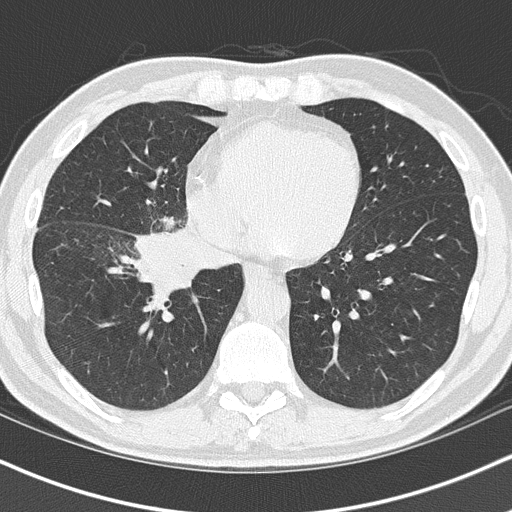
Low-dose screening chest CT, one axial slice; position 48 of 151 along the scan axis; lung window (W 1500 / L -600 HU); 2 mm slice thickness; 512 × 512 image matrix.
Outlined on this slice (expert manual segmentation):
- lesion 1 (tumor, hilum of right lung): bounding box <138,216,198,290> (left, top, right, bottom; pixels)